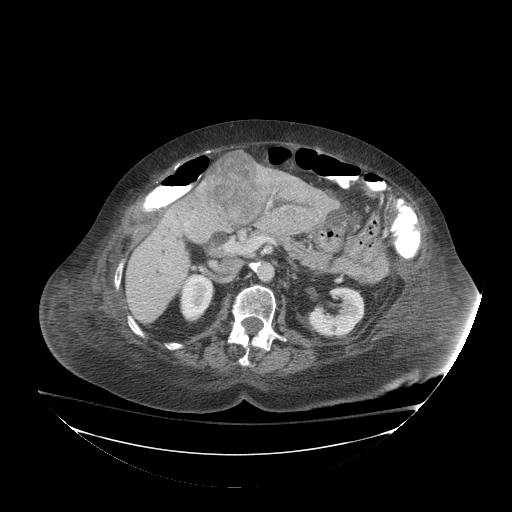
Contrast-enhanced abdominal CT (liver protocol), one axial slice; slice 36 of 81 in the series (ordered by position); soft-tissue window (W 400 / L 40 HU); 2.5 mm slice thickness; 512 × 512 image matrix. Case-level facts recorded for this patient, not image findings: diagnosis: hepatocellular carcinoma (patient treated with transarterial chemoembolisation; whether this scan precedes or follows treatment is not stated here); TNM stage (as recorded): Stage-I; Child-Pugh class: B; tumour differentiation: well-moderately differentiated.
Structures marked on this image (semi-automatic segmentation, software-assisted and operator-edited):
- liver parenchyma outside the tumour (the mass and vessels are separate outlines, so this box may not span the whole liver): bounding box (x1, y1, x2, y2) in pixels: (126, 204, 318, 324)
- mass: (203, 149, 273, 220)